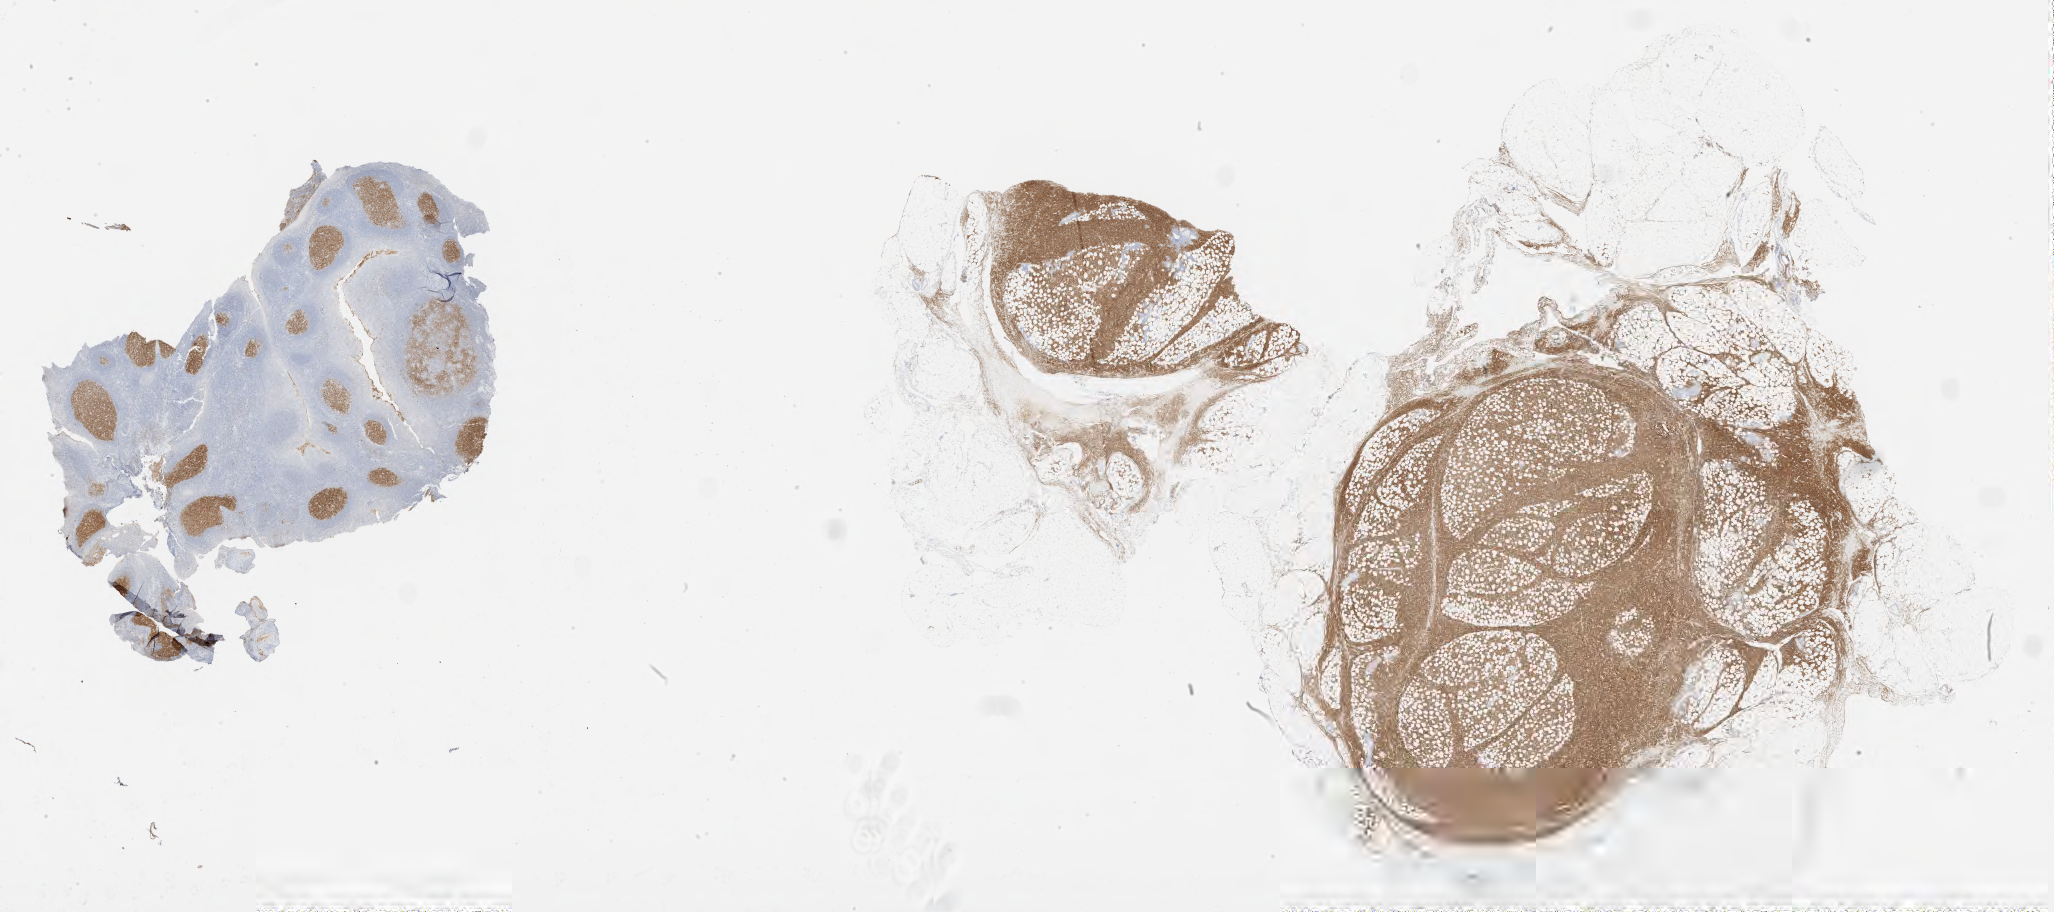
IHC for CD10, whole-slide image, whole scanned area (about 33.0 x 14.6 mm) shown as a low-resolution overview. Specimen: tumor tissue. Male patient, age 24 years.
Histologic diagnosis: Burkitt lymphoma, NOS.